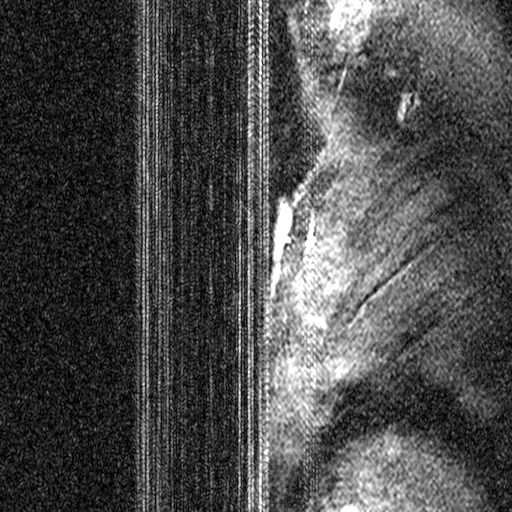
Breast MRI (dynamic contrast-enhanced), one sagittal slice. Slice 34 of 44 in the series (ordered by position). Dynamic contrast-enhanced study with each time point stored as its own series, time point 2 of 3 at this slice position (early post-contrast, ordered by acquisition time). 1.5 T. TE 4.5 ms, TR 11 ms. 3 mm slice thickness. 512 × 512 image matrix, field of view 200 × 200 mm. Female patient, age 44 years. From the clinical record (not read from this slice): setting: breast cancer imaged before/during neoadjuvant chemotherapy; receptor status: HR-positive, HER2-negative.
Structures marked on this image (semi-automatic segmentation, software-assisted and operator-edited):
- analysis volume of interest (the breast-tissue region the enhancement analysis was run in; not a lesion): bounding box (x1, y1, x2, y2) in pixels: (206, 164, 319, 299)
- tumour enhancement mask (voxels above the 90 % enhancement threshold inside the analysis volume of interest): (259, 165, 313, 257)